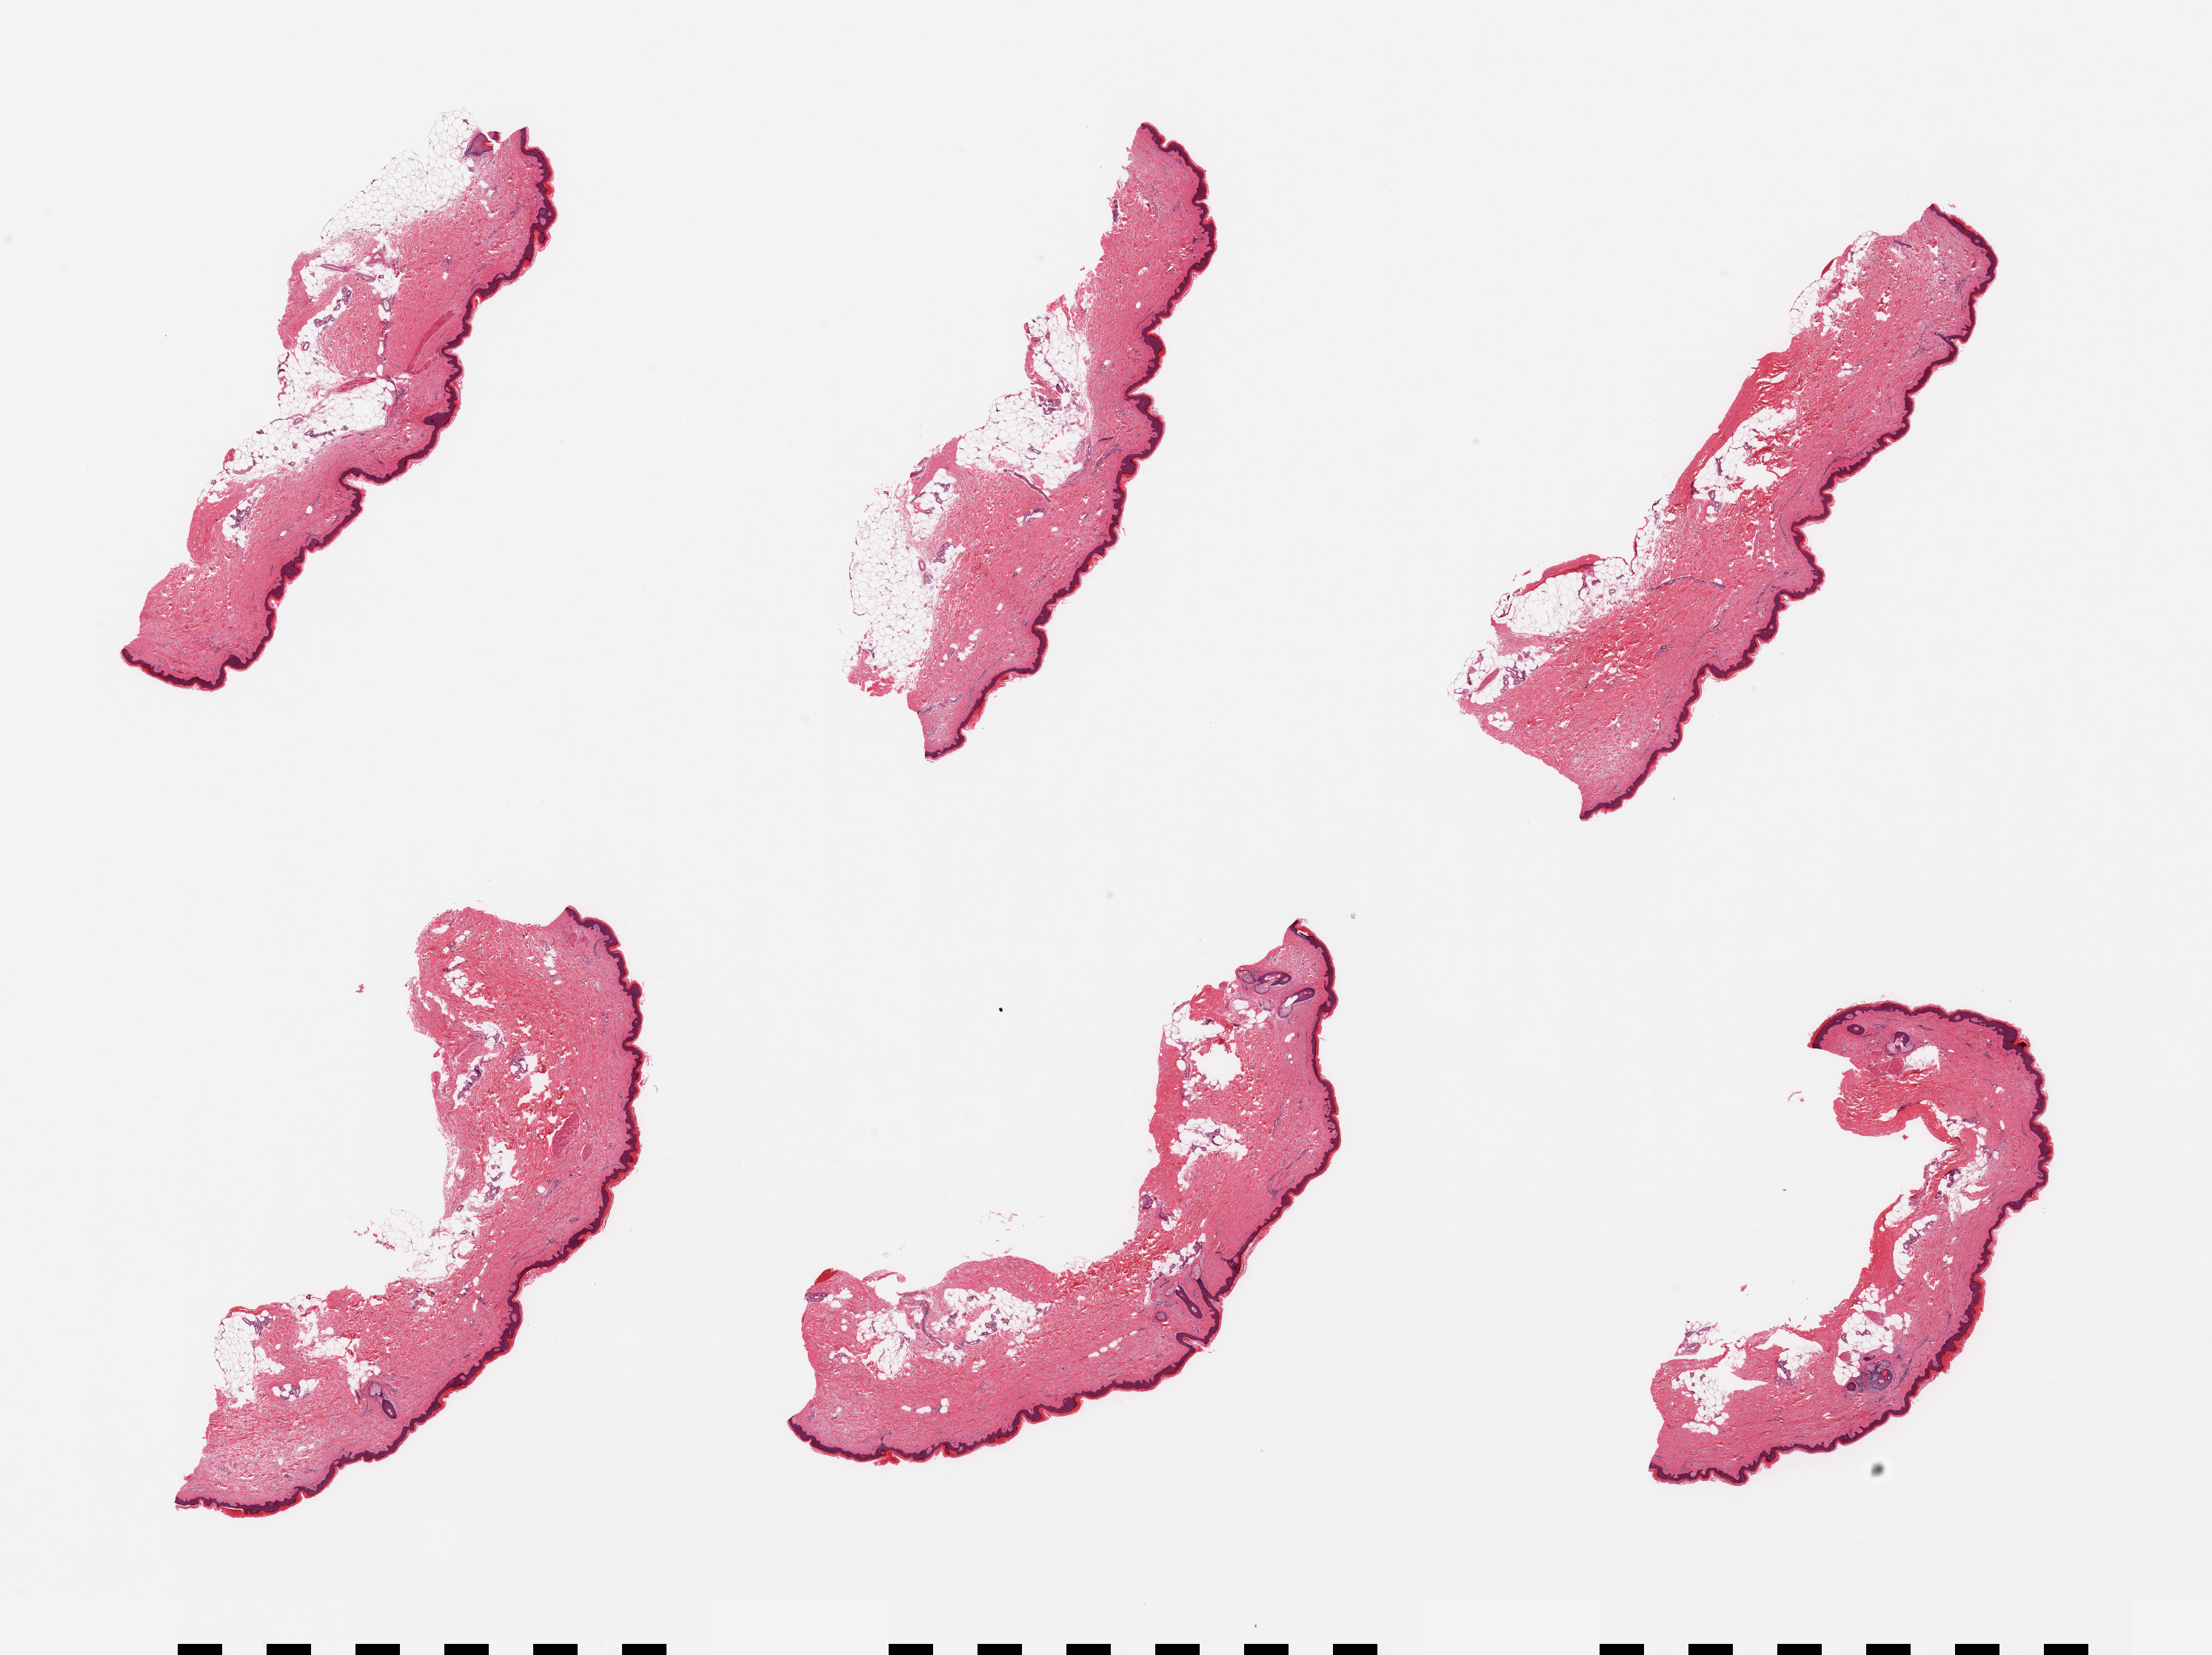
Whole-slide image, haematoxylin and eosin stain, brightfield, shown as a low-resolution overview of the whole scanned area (about 23.6 x 17.7 mm). PAXgene-fixed paraffin-embedded (PFPE) section. Sampled site (target tissue): skin of lower leg. Donor tissue sample. Female donor.
Pathologist's review note for this sample: 6 pieces, dermal fat up to ~1mm; squamous epithelium is ~ 40 microns.